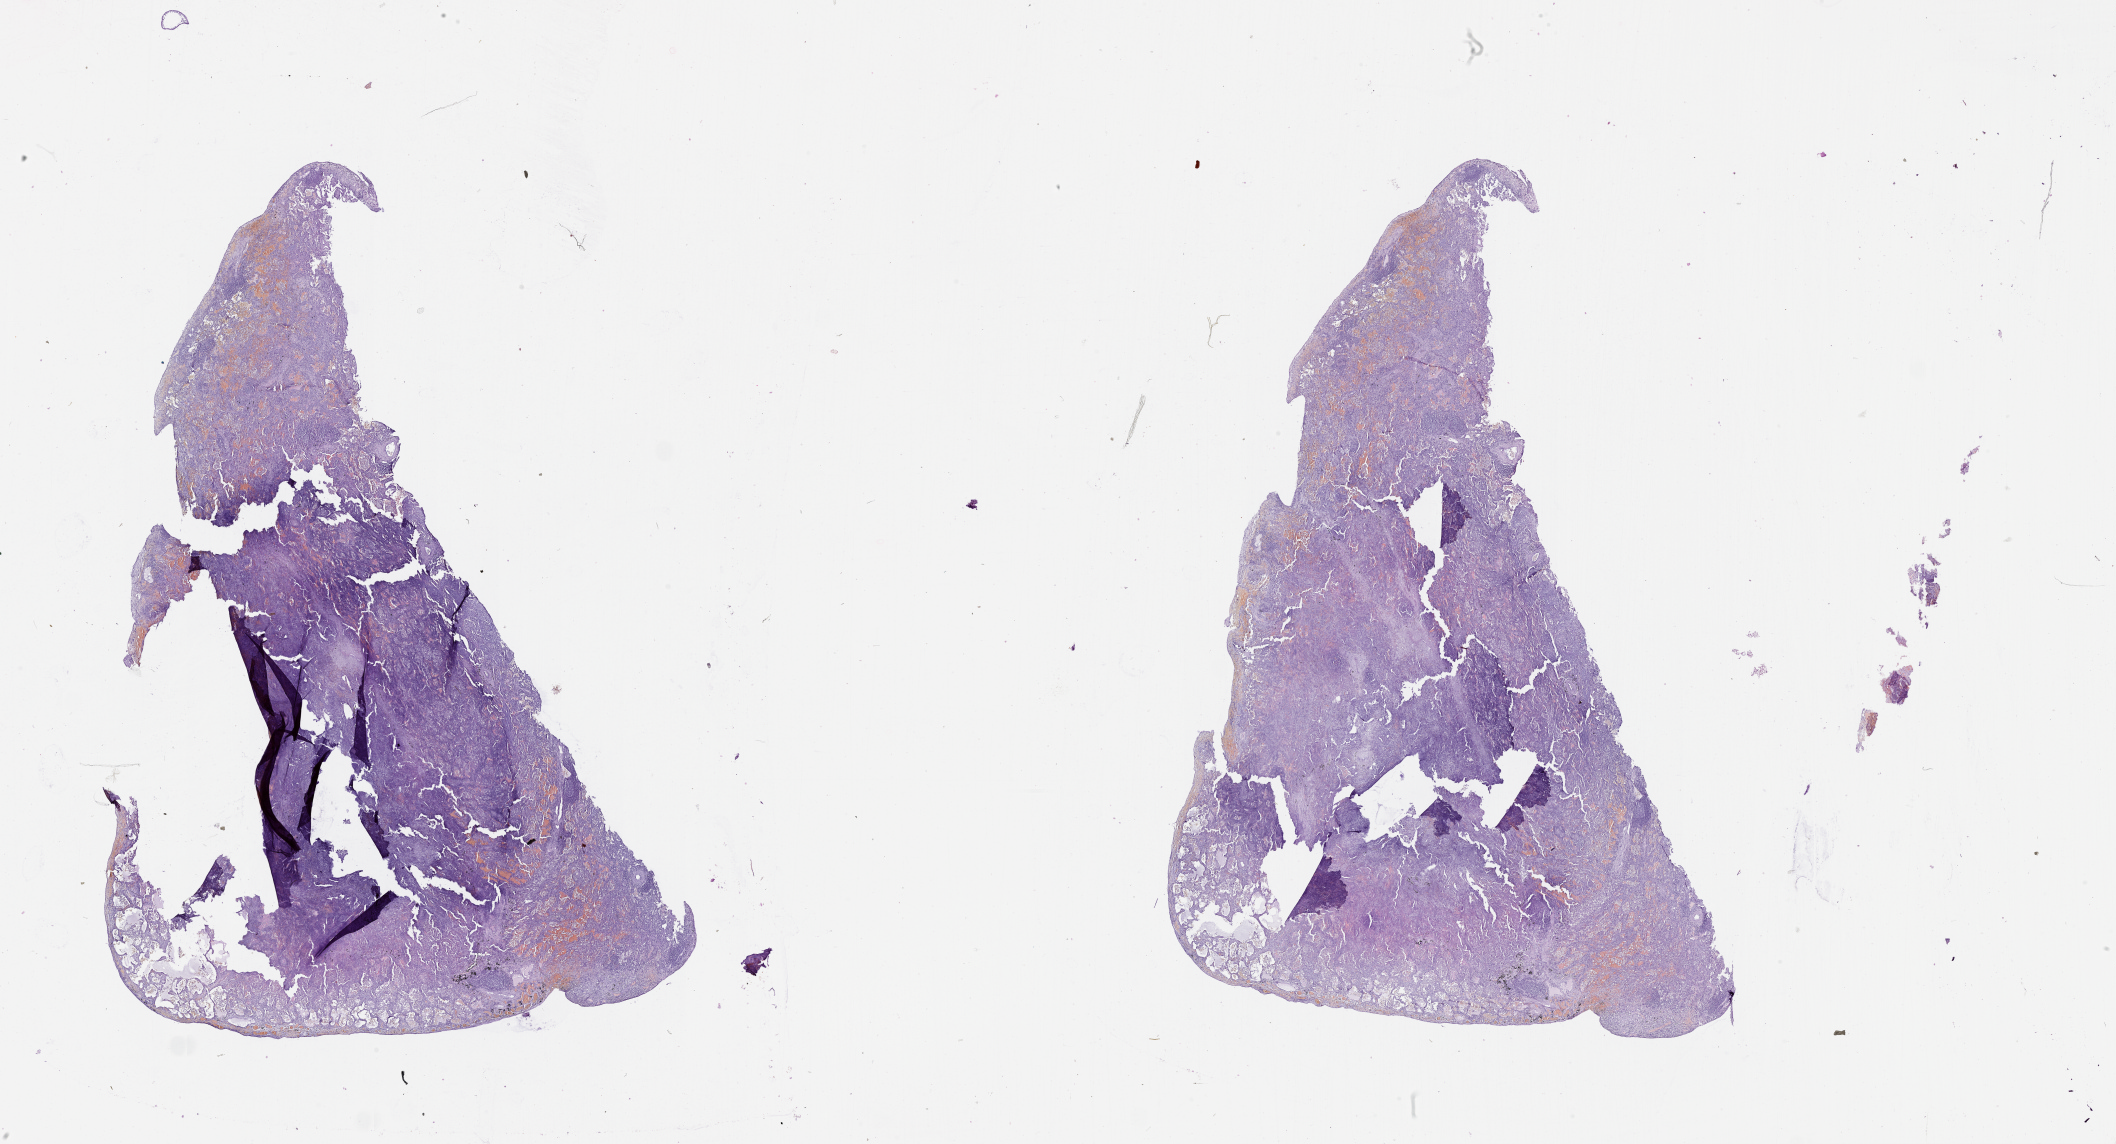
Whole-slide histology image, H&E, shown as a low-resolution overview of the whole scanned area (about 34.1 x 18.4 mm, from a 20x scan); lung, tumour tissue. Male, 70 y/o.
Patient diagnosis (cohort enrolment): squamous cell carcinoma (lung).